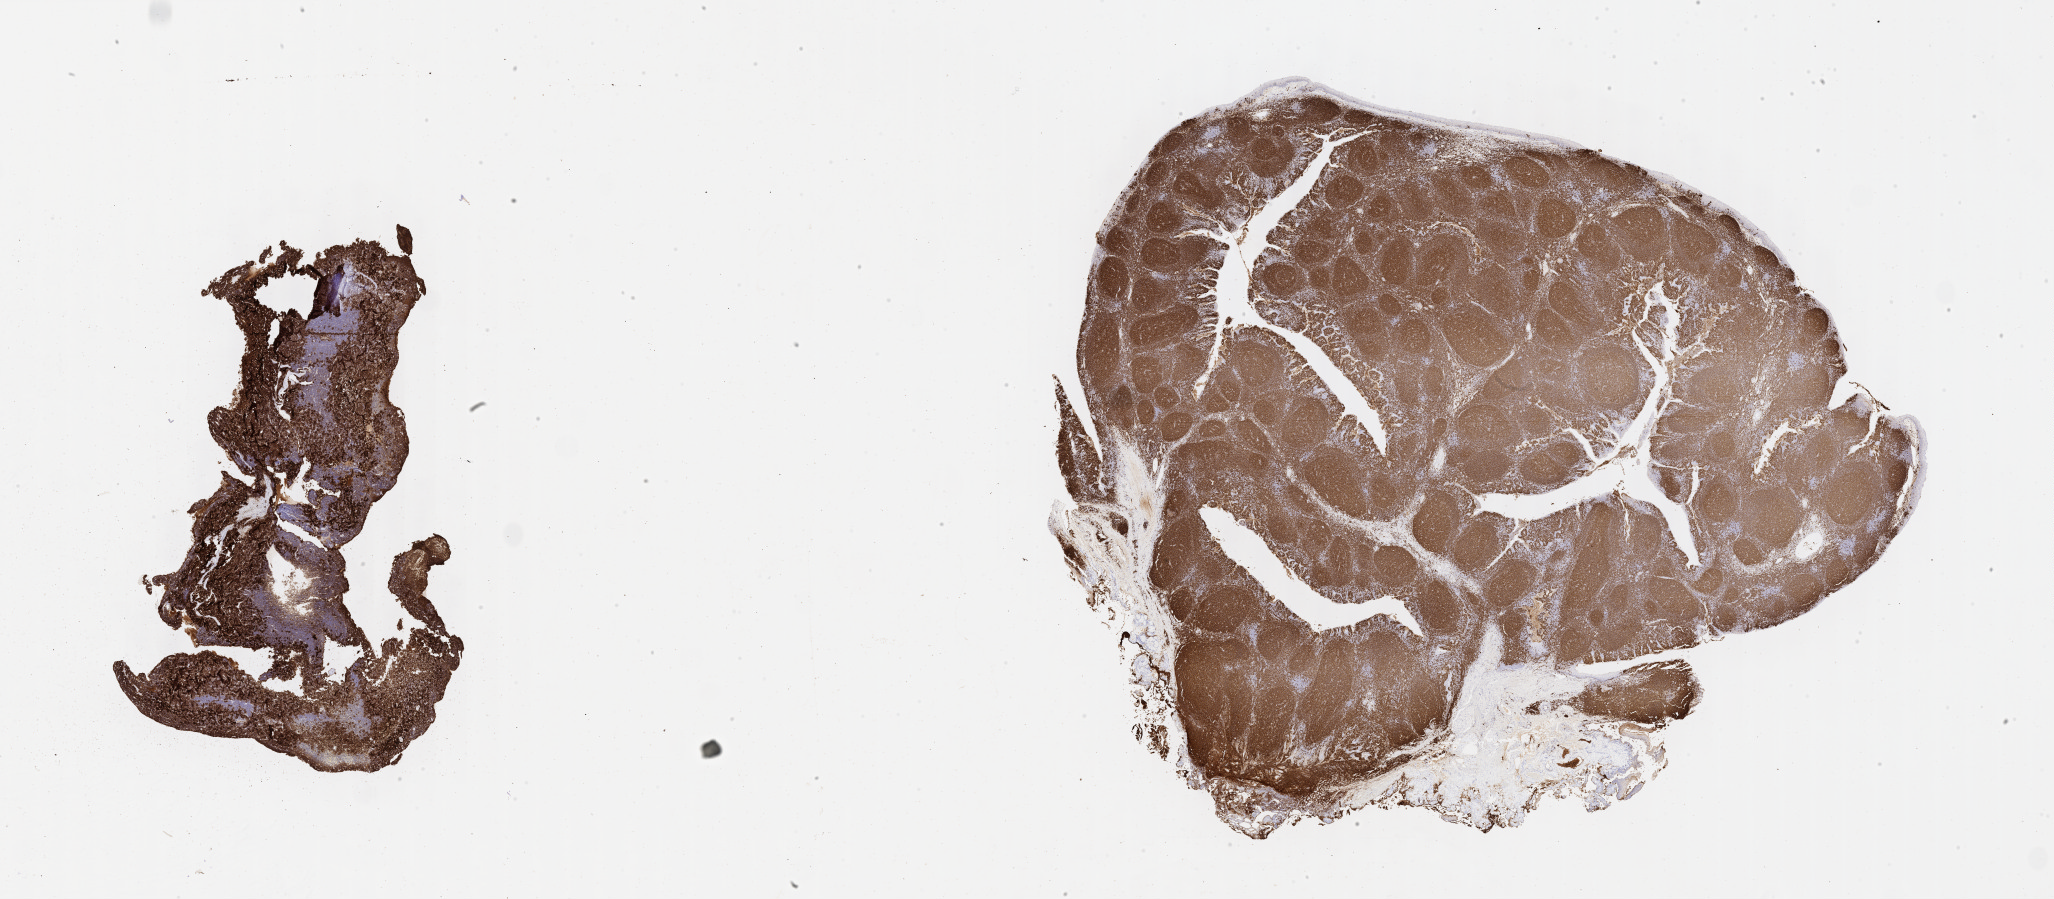
IHC for CD20, whole-slide image, shown as a low-resolution overview of the whole scanned area (about 33.2 x 14.5 mm); specimen: tumor tissue; anatomic site: cranium. Patient: female, age 10 years.
Histologic diagnosis: Burkitt lymphoma, NOS.